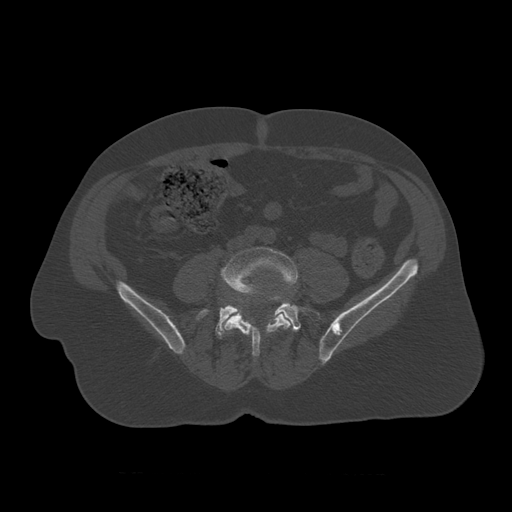
CT including the spine, one axial slice; reconstruction kernel STANDARD; 120 kVp; bone window (W 1800 / L 400 HU); 1.25 mm slice thickness; 512 × 512 image matrix, field of view 405 × 405 mm. Patient age 75 years. From the clinical record (not read from this slice): primary cancer: prostate.
Annotated regions visible in this slice (semi-automatic segmentation, software-assisted and operator-edited):
- L4 vertebra: box from (x=221, y=248) to (x=299, y=357) px
- L5 vertebra: (x=196, y=295)–(x=321, y=339)